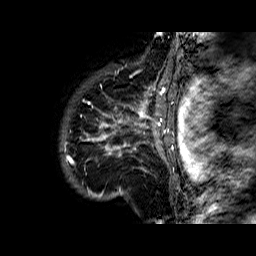
Breast MRI (dynamic contrast-enhanced), one sagittal slice; dynamic contrast-enhanced series, time point 2 of 6 at this slice position (early post-contrast); 1.5 T; TE 6.3 ms, TR 32.4 ms; 4 mm slice thickness; 256 × 256 image matrix, field of view 200 × 200 mm. Female patient. From the clinical record (not read from this slice): setting: breast cancer imaged before/during neoadjuvant chemotherapy; receptor status: HR-positive, HER2-negative.
Outlined on this slice (semi-automatic segmentation, software-assisted and operator-edited):
- analysis volume of interest (the breast-tissue region the enhancement analysis was run in; not a lesion): bounding box (x1, y1, x2, y2) in pixels: (68, 72, 177, 183)
- tumour enhancement mask (voxels above the 100 % enhancement threshold inside the analysis volume of interest): (68, 72, 174, 169)